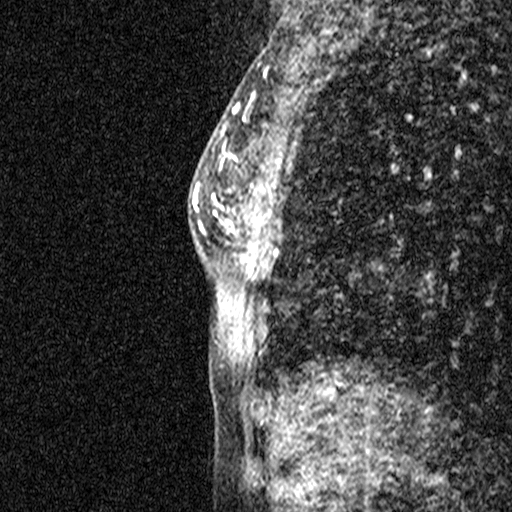
Breast MRI (dynamic contrast-enhanced), one sagittal slice. Slice 20 of 44 in the series (ordered by position). Dynamic contrast-enhanced study with each time point stored as its own series, time point 2 of 3 at this slice position (early post-contrast, ordered by acquisition time). 1.5 T. TE 4.5 ms, TR 11 ms. 3 mm slice thickness. 512 × 512 image matrix, field of view 200 × 200 mm. Female patient, age 44 years. From the clinical record (not read from this slice): setting: breast cancer imaged before/during neoadjuvant chemotherapy; receptor status: HR-positive, HER2-negative.
Annotated regions visible in this slice (semi-automatically segmented with operator editing):
- analysis volume of interest (the breast-tissue region the enhancement analysis was run in; not a lesion): bounding box (x1, y1, x2, y2) in pixels: (218, 118, 341, 291)
- tumour enhancement mask (voxels above the 90 % enhancement threshold inside the analysis volume of interest): (219, 123, 278, 226)